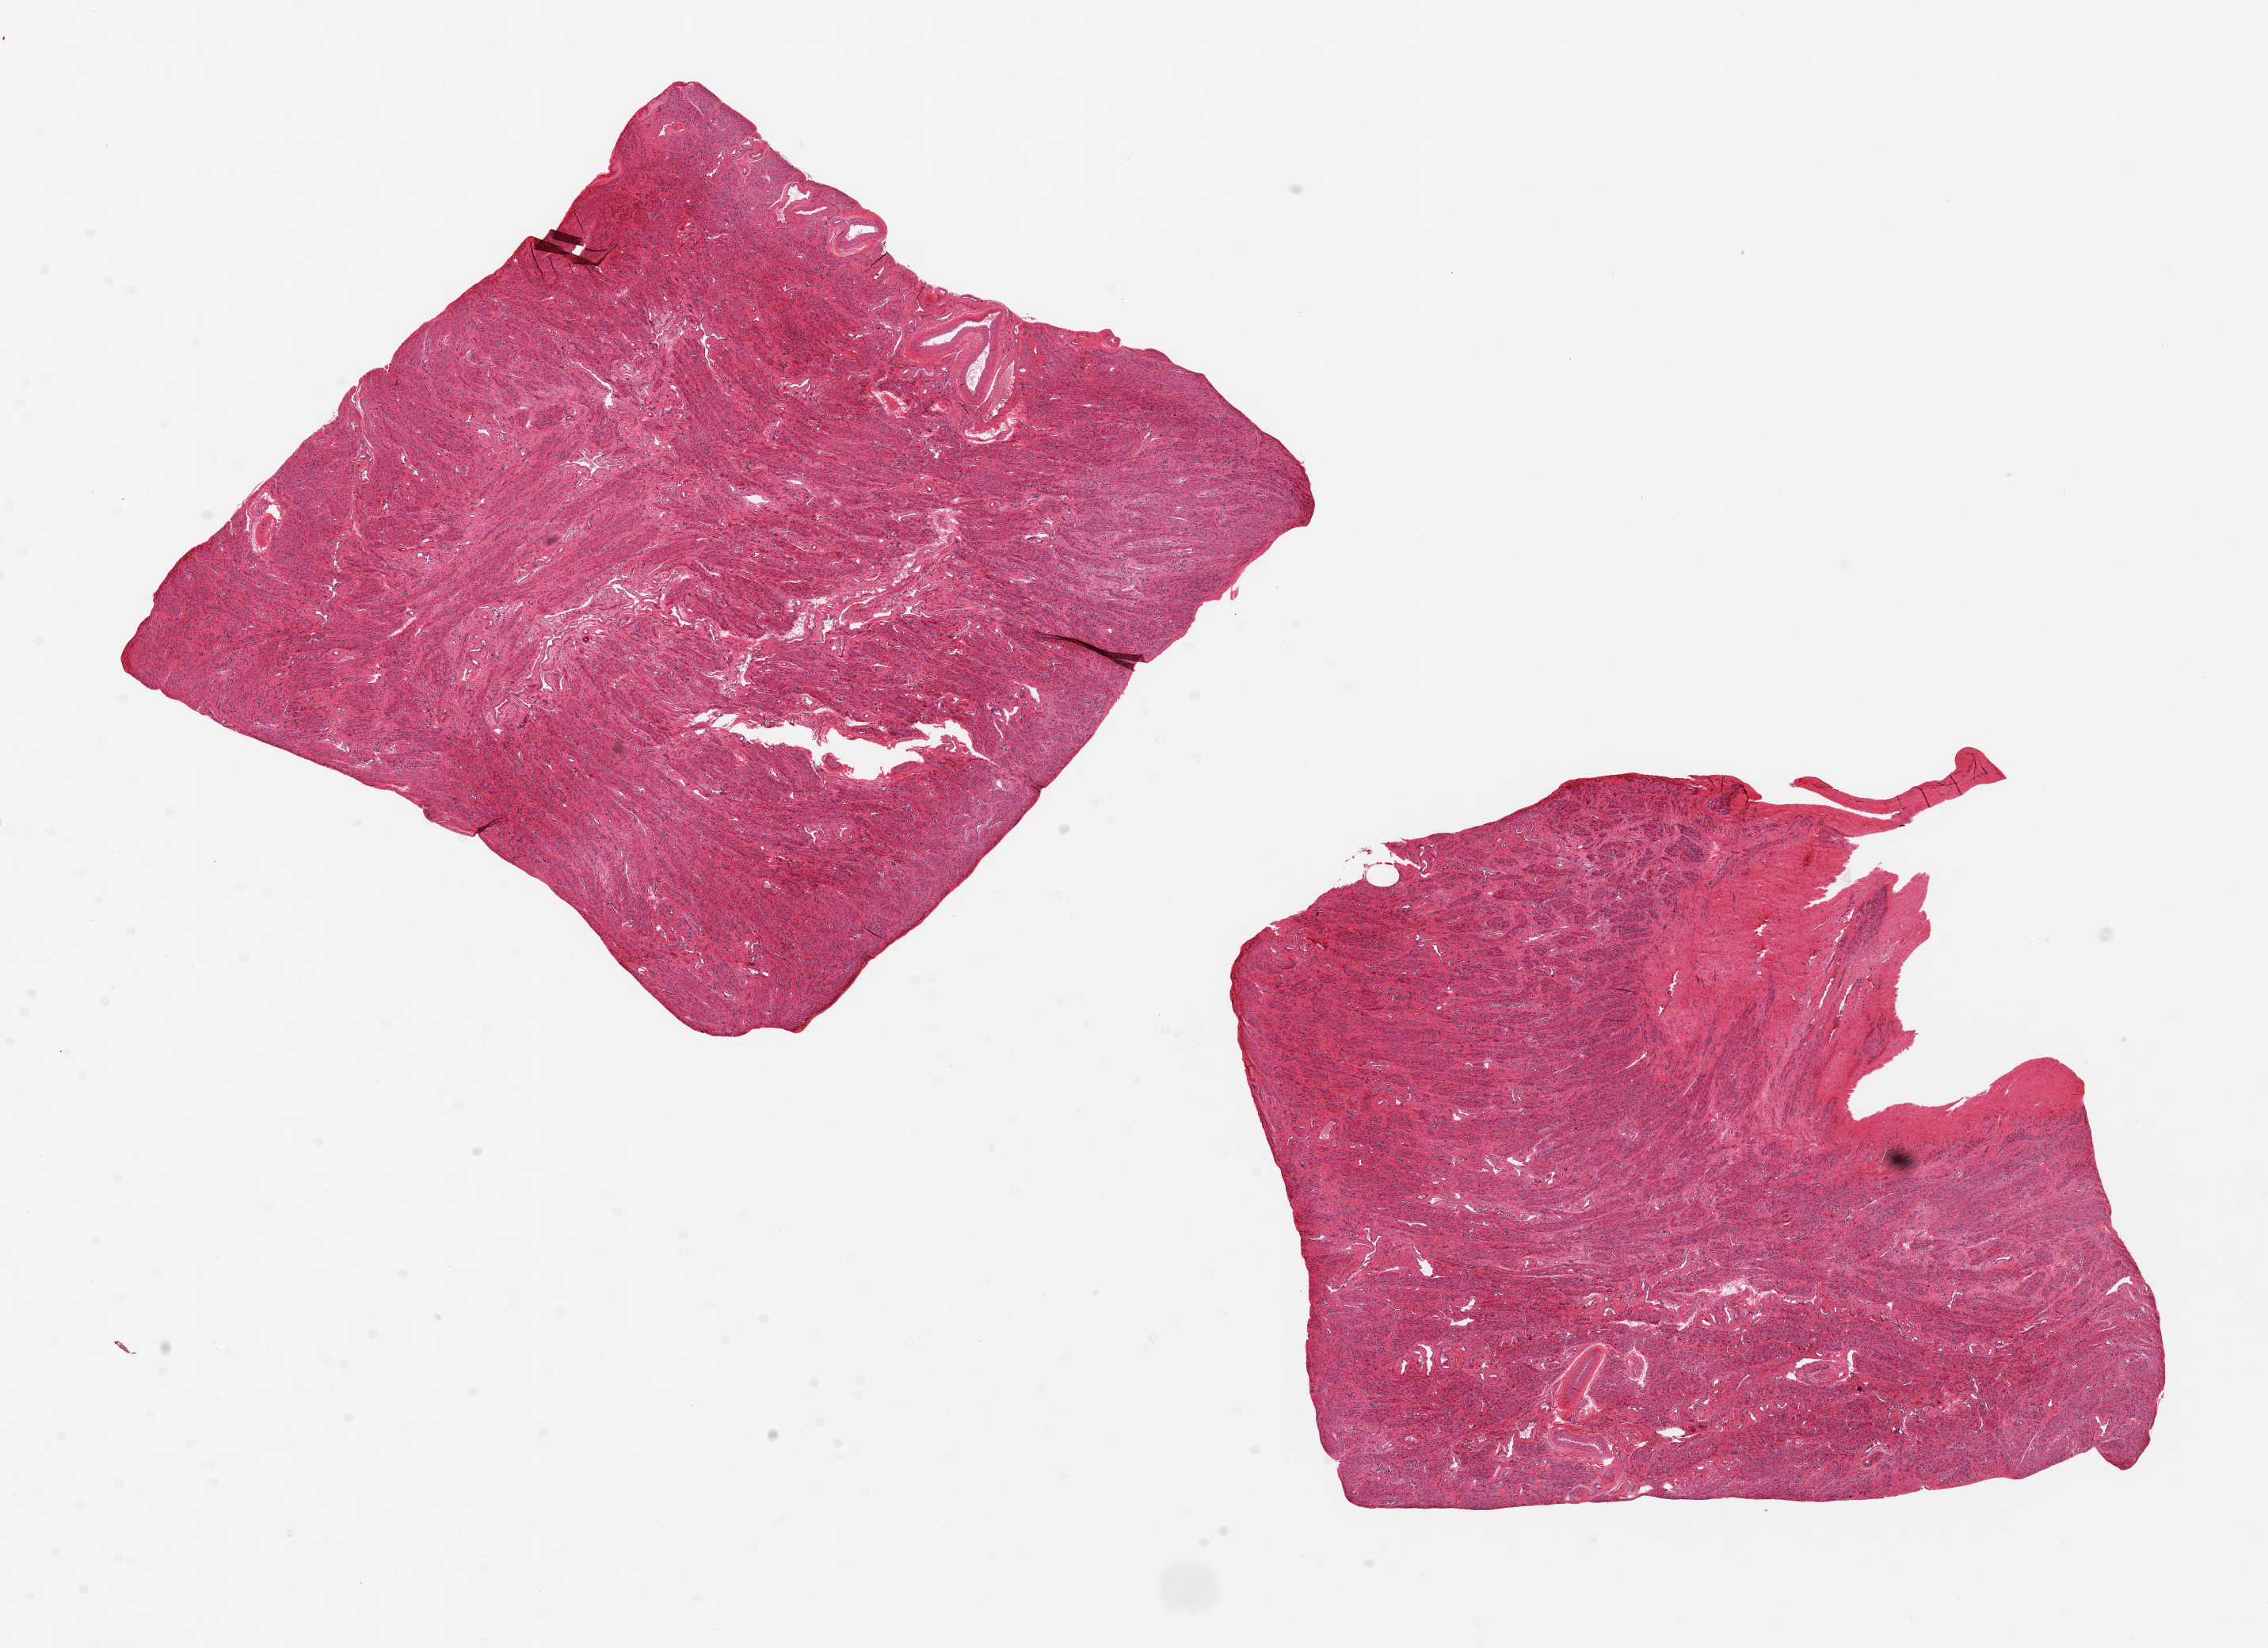
H&E whole-slide image — low-resolution overview of the scanned area, about 22.6 x 16.4 mm. PAXgene-fixed, paraffin-embedded tissue. Sampled site (target tissue): uterus. Donor tissue sample.
Review note (as recorded): 2 pieces 8x7 mm; all myometrium, no endometrium.